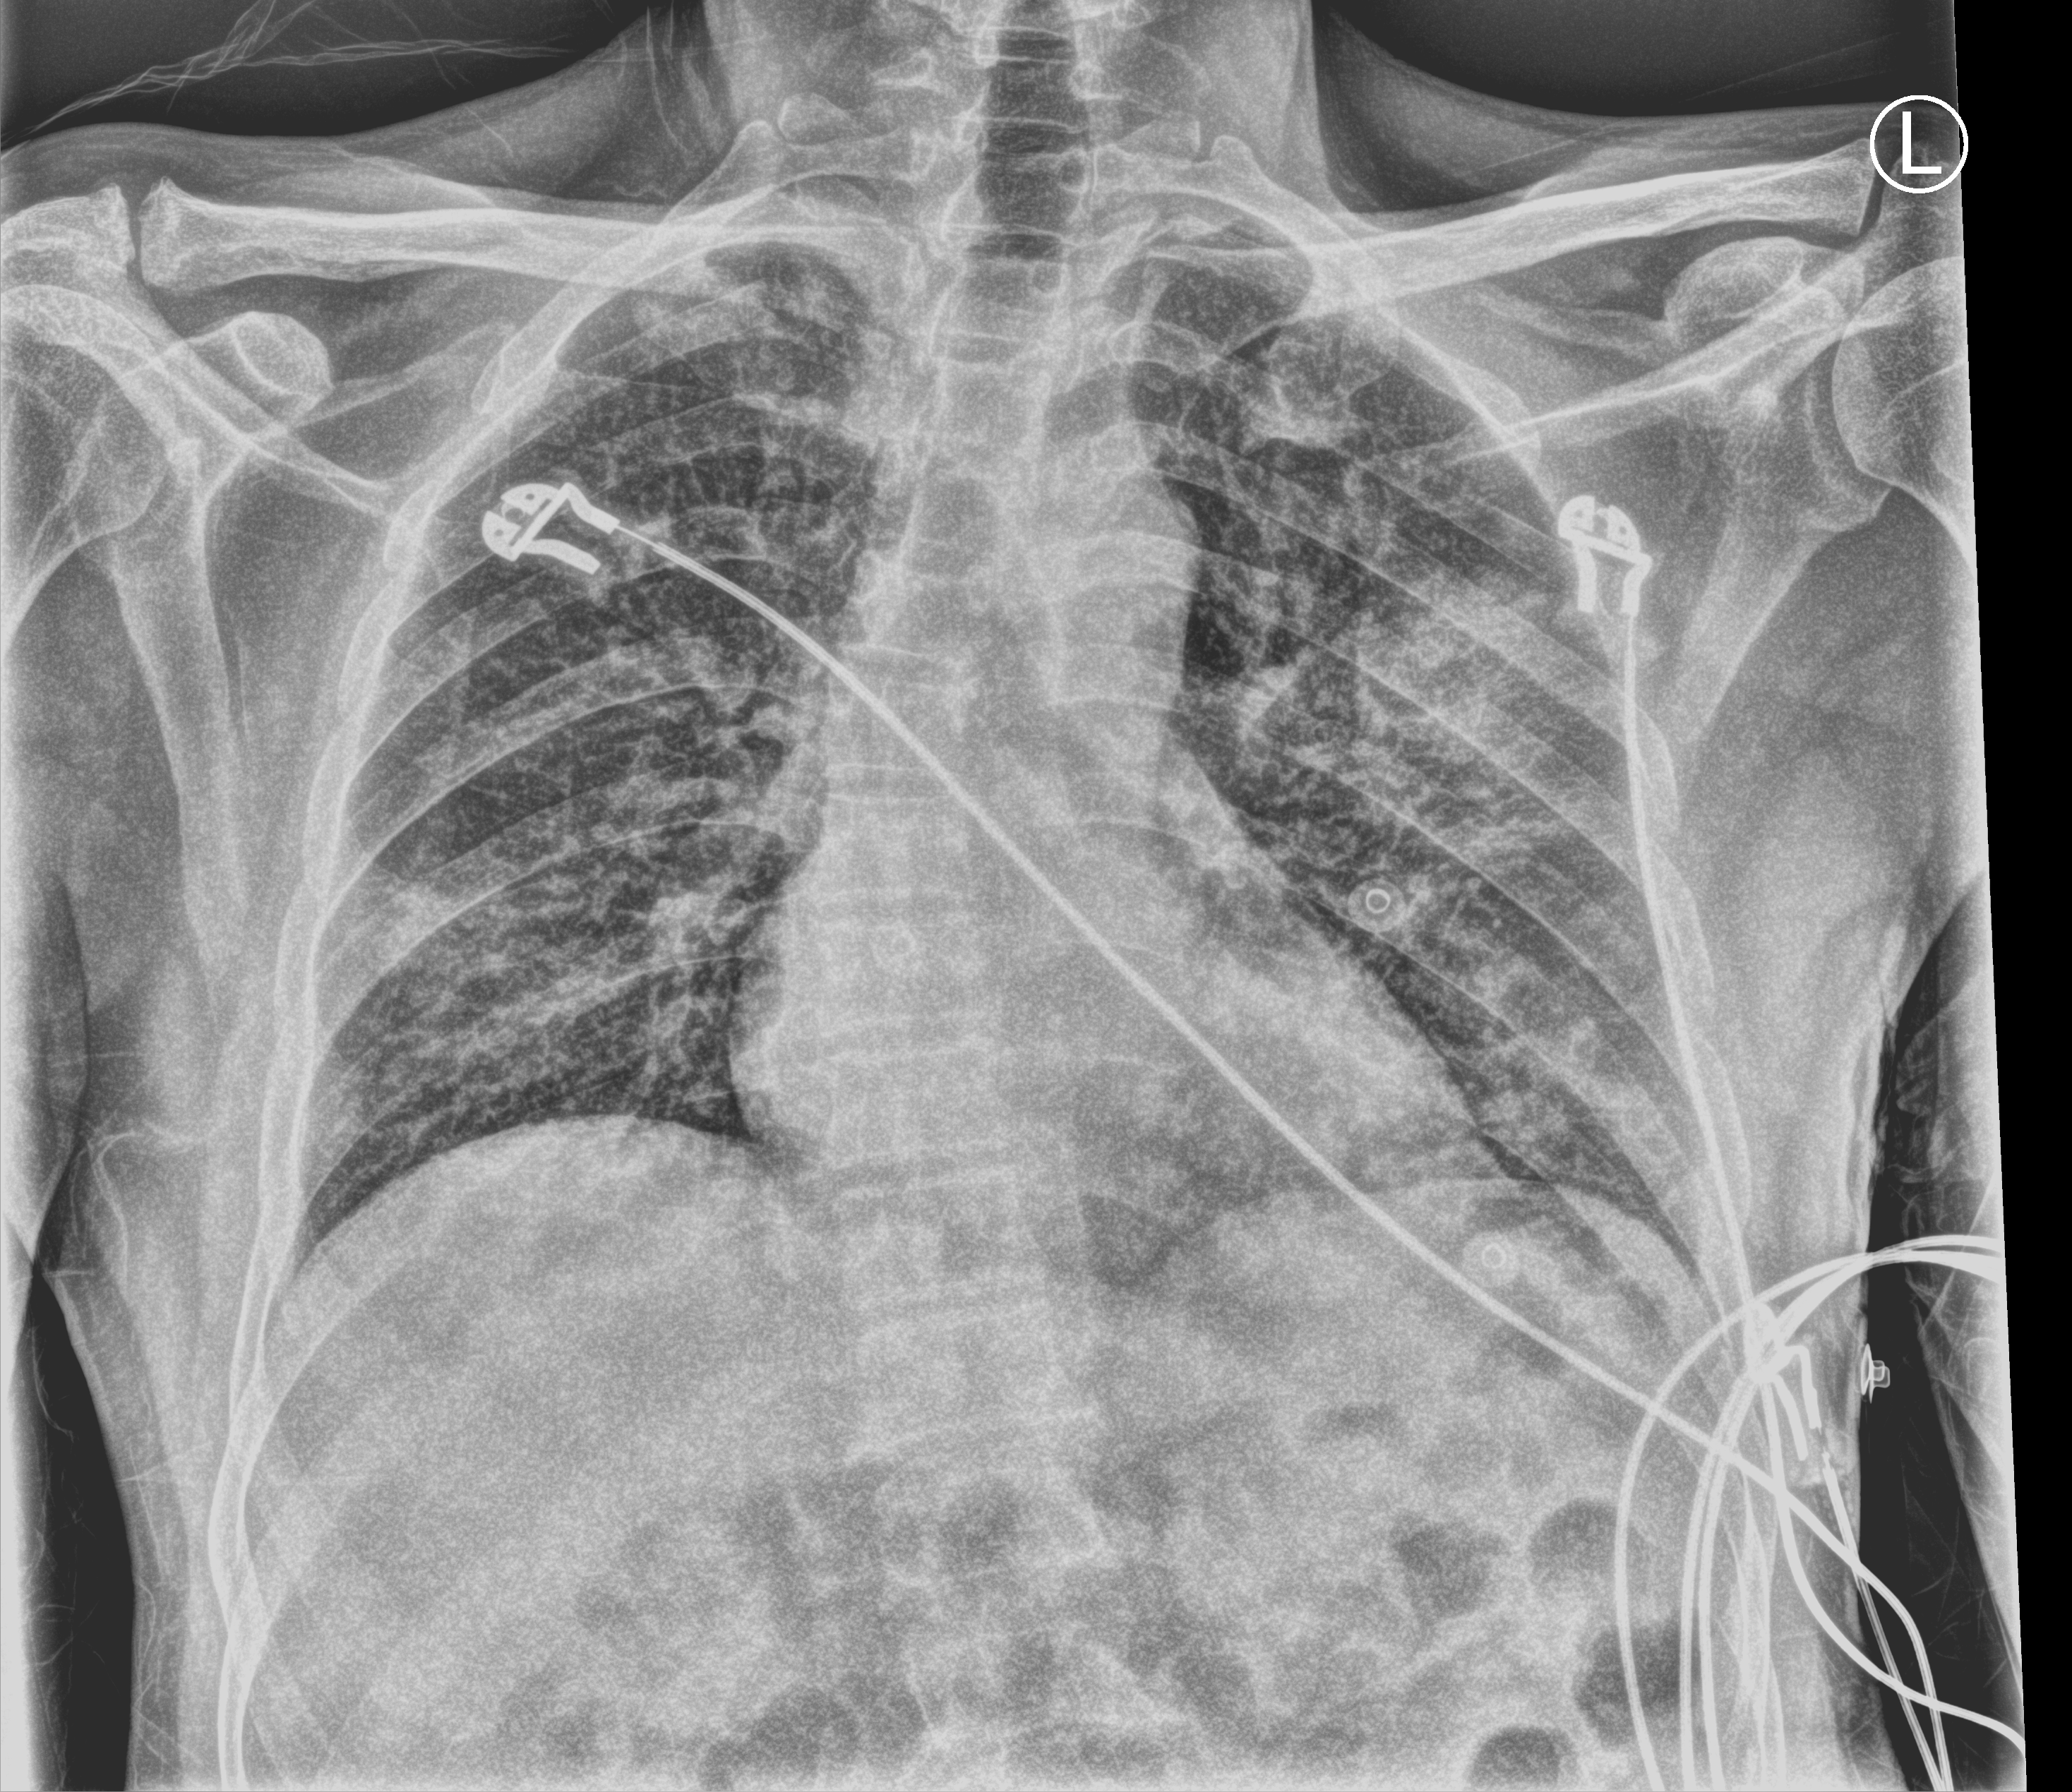
Bedside chest radiograph (computed radiography); anteroposterior (AP) projection. Patient hospitalised with COVID-19; male, aged 60–74 years.
From the hospital-stay record, not from the radiograph (when in the stay this image was taken is not recorded): mechanically ventilated during this hospital stay: no; length of hospital stay: 1 day.